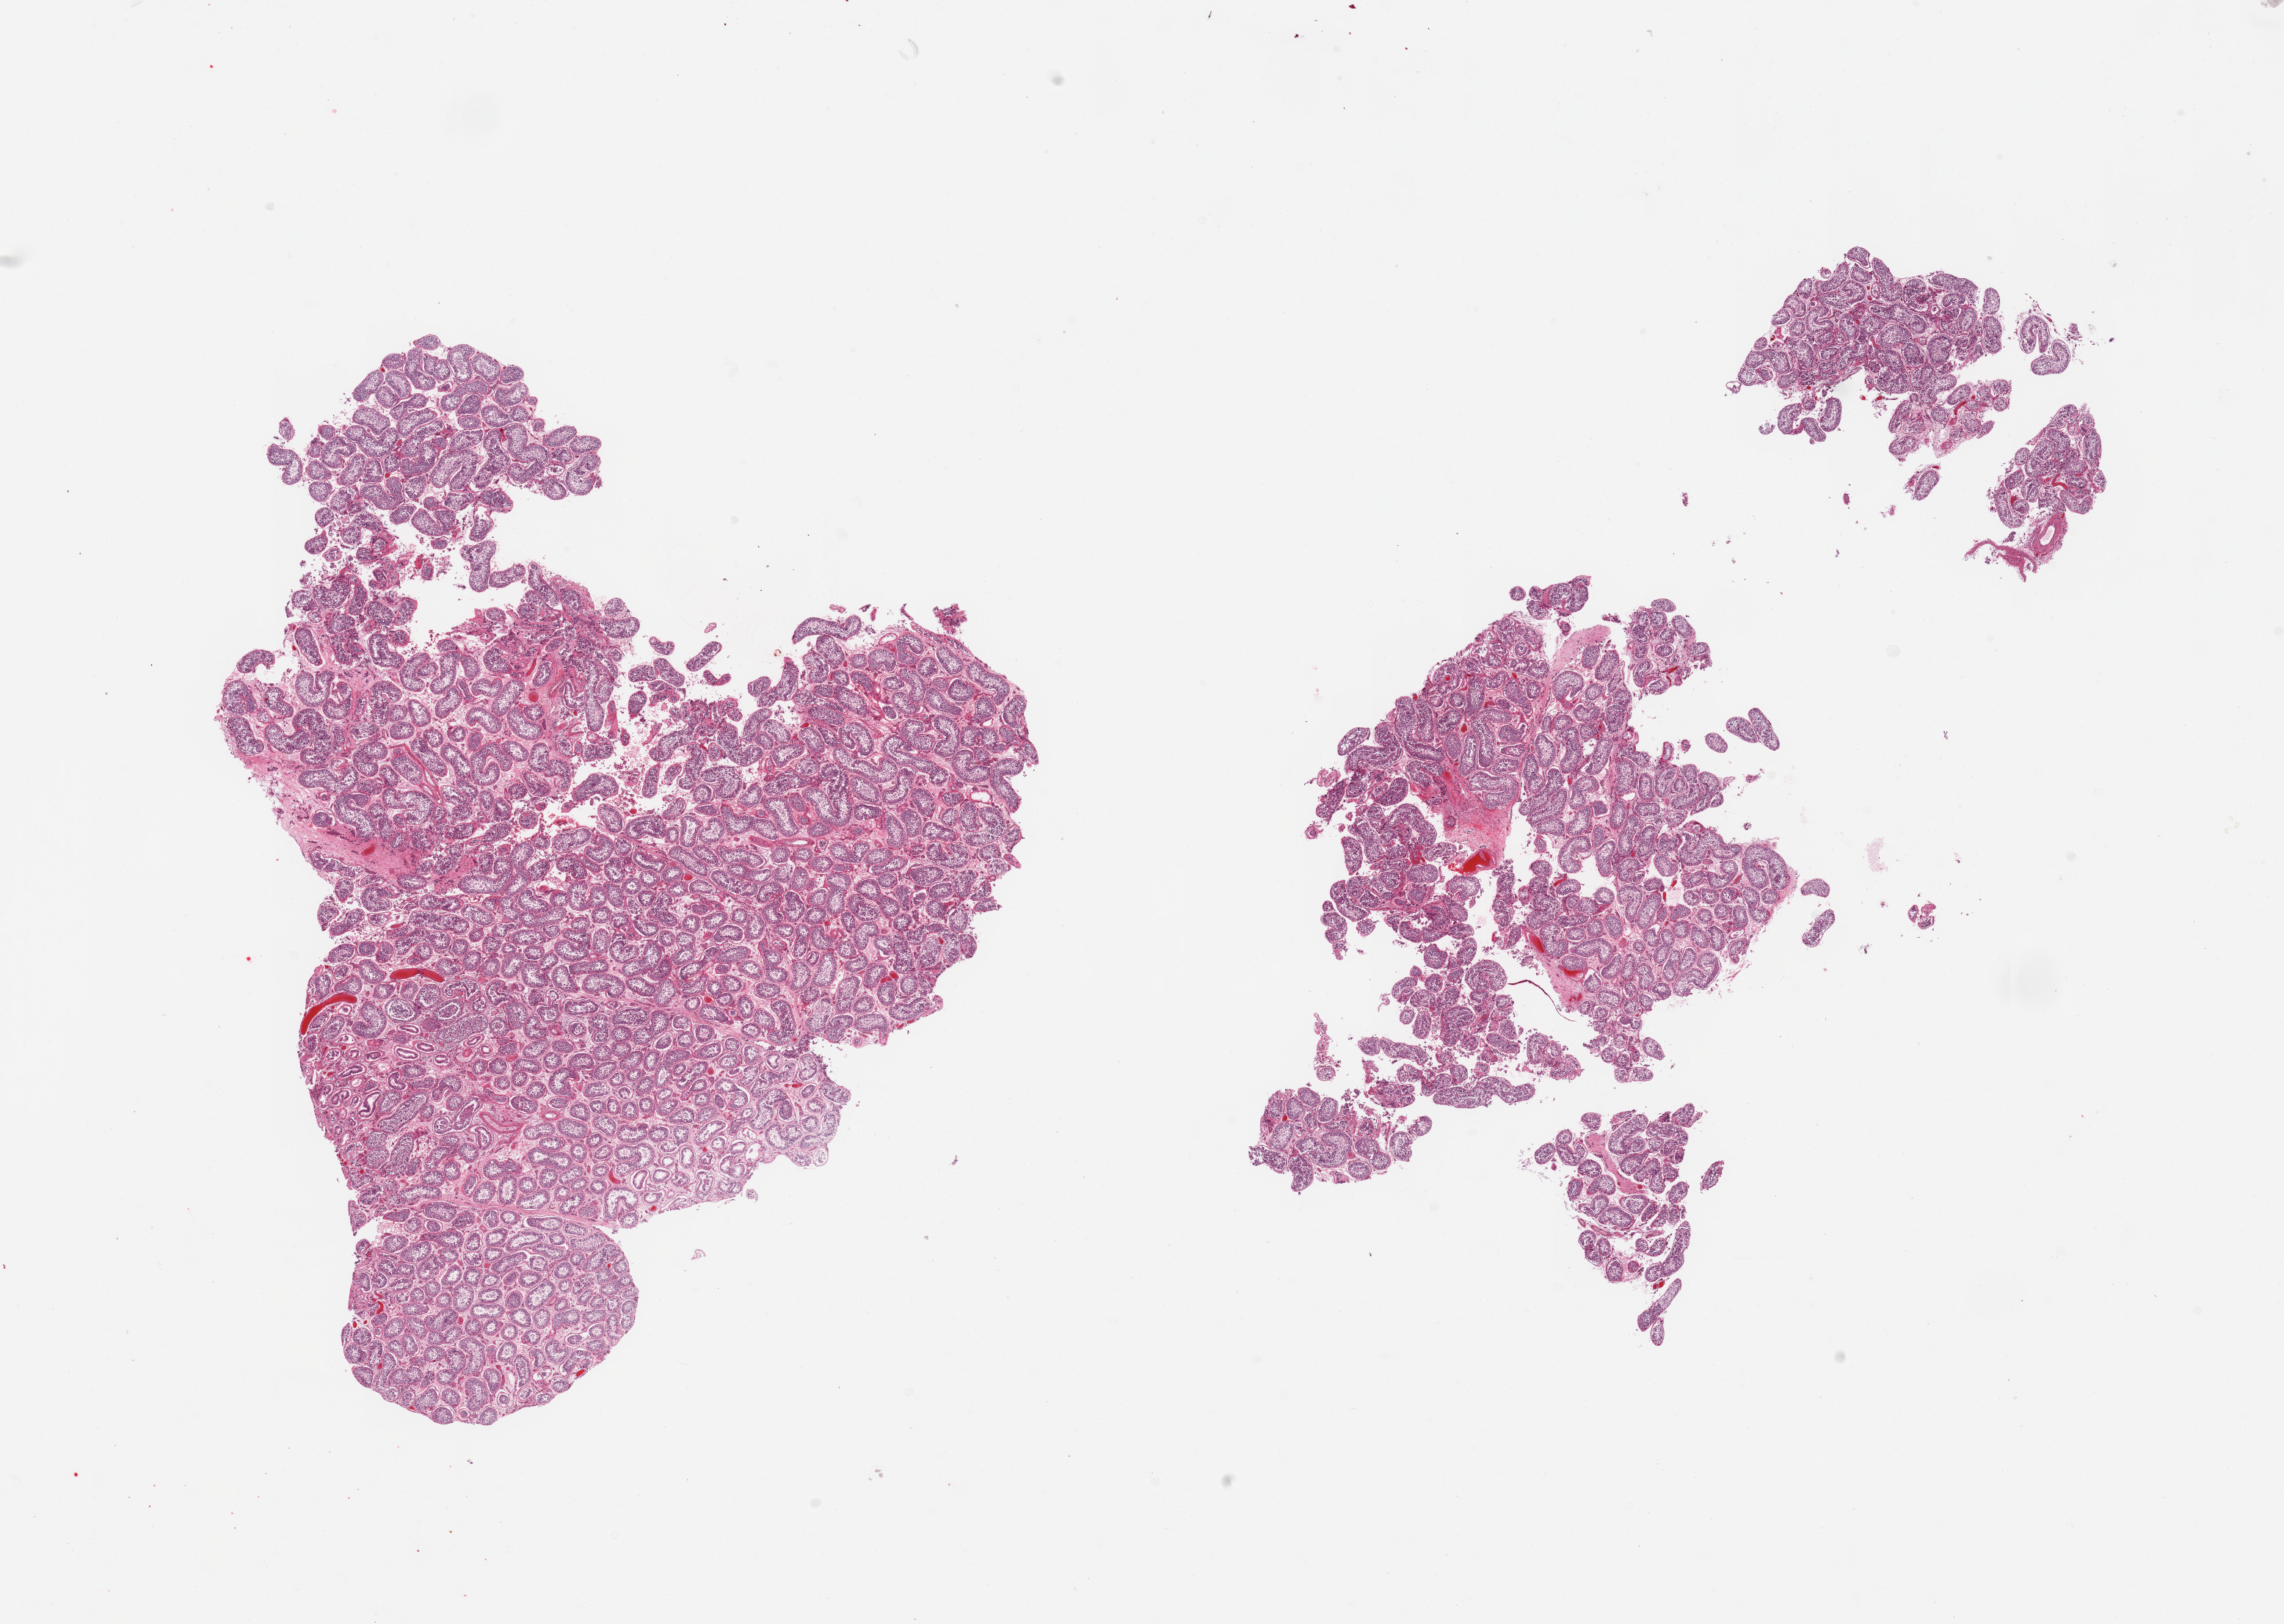
Digitized haematoxylin and eosin-stained section, brightfield — shown as a low-resolution overview of the whole scanned area (about 24.6 x 17.5 mm, acquisition: 20x scan). PAXgene-fixed paraffin-embedded (PFPE) section. Section of testis (target tissue). Tissue donor sample. Donor: male.
* pathologist's review note for this sample: 2 fragmented pieces; active spermatogenesis